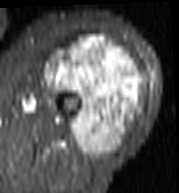
MRI of an extremity soft-tissue mass, one axial slice; slice 58 of 103 in the series (ordered by position); STIR; MR volume resampled by the dataset authors to the PET/CT grid (not the native acquisition matrix); 3.27 mm slice thickness; 179 × 193 image matrix. Female patient. From the clinical record (not read from this slice): histological type: undifferentiated – high grade; grade: high; site of the primary tumour: left thigh.
Structures marked on this image (expert contour drawn on MRI and transferred to this co-registered scan by the dataset authors):
- gross tumour volume including surrounding oedema: bounding box [x1, y1, x2, y2] px = [45, 37, 142, 159]
- gross tumour volume (mass): [45, 37, 142, 159]